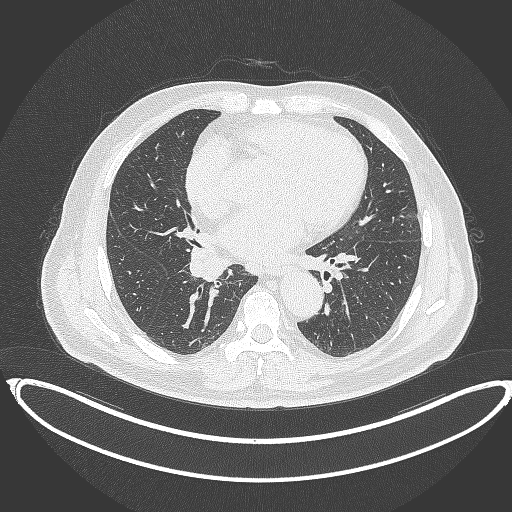
Chest CT, one axial slice; position 193 of 387 along the scan axis; lung window (W 1500 / L -600 HU); 1 mm slice thickness; 512 × 512 image matrix, field of view 448 × 448 mm. Patient: male, 61 years. From the clinical record (not read from this slice): clinical TNM (as recorded): T1b N1 M0.
Annotated regions visible in this slice (bounding box drawn by a radiologist):
- lung tumour (recorded histology: squamous cell carcinoma): bounding box (x1, y1, x2, y2) in pixels: (187, 242, 234, 284)